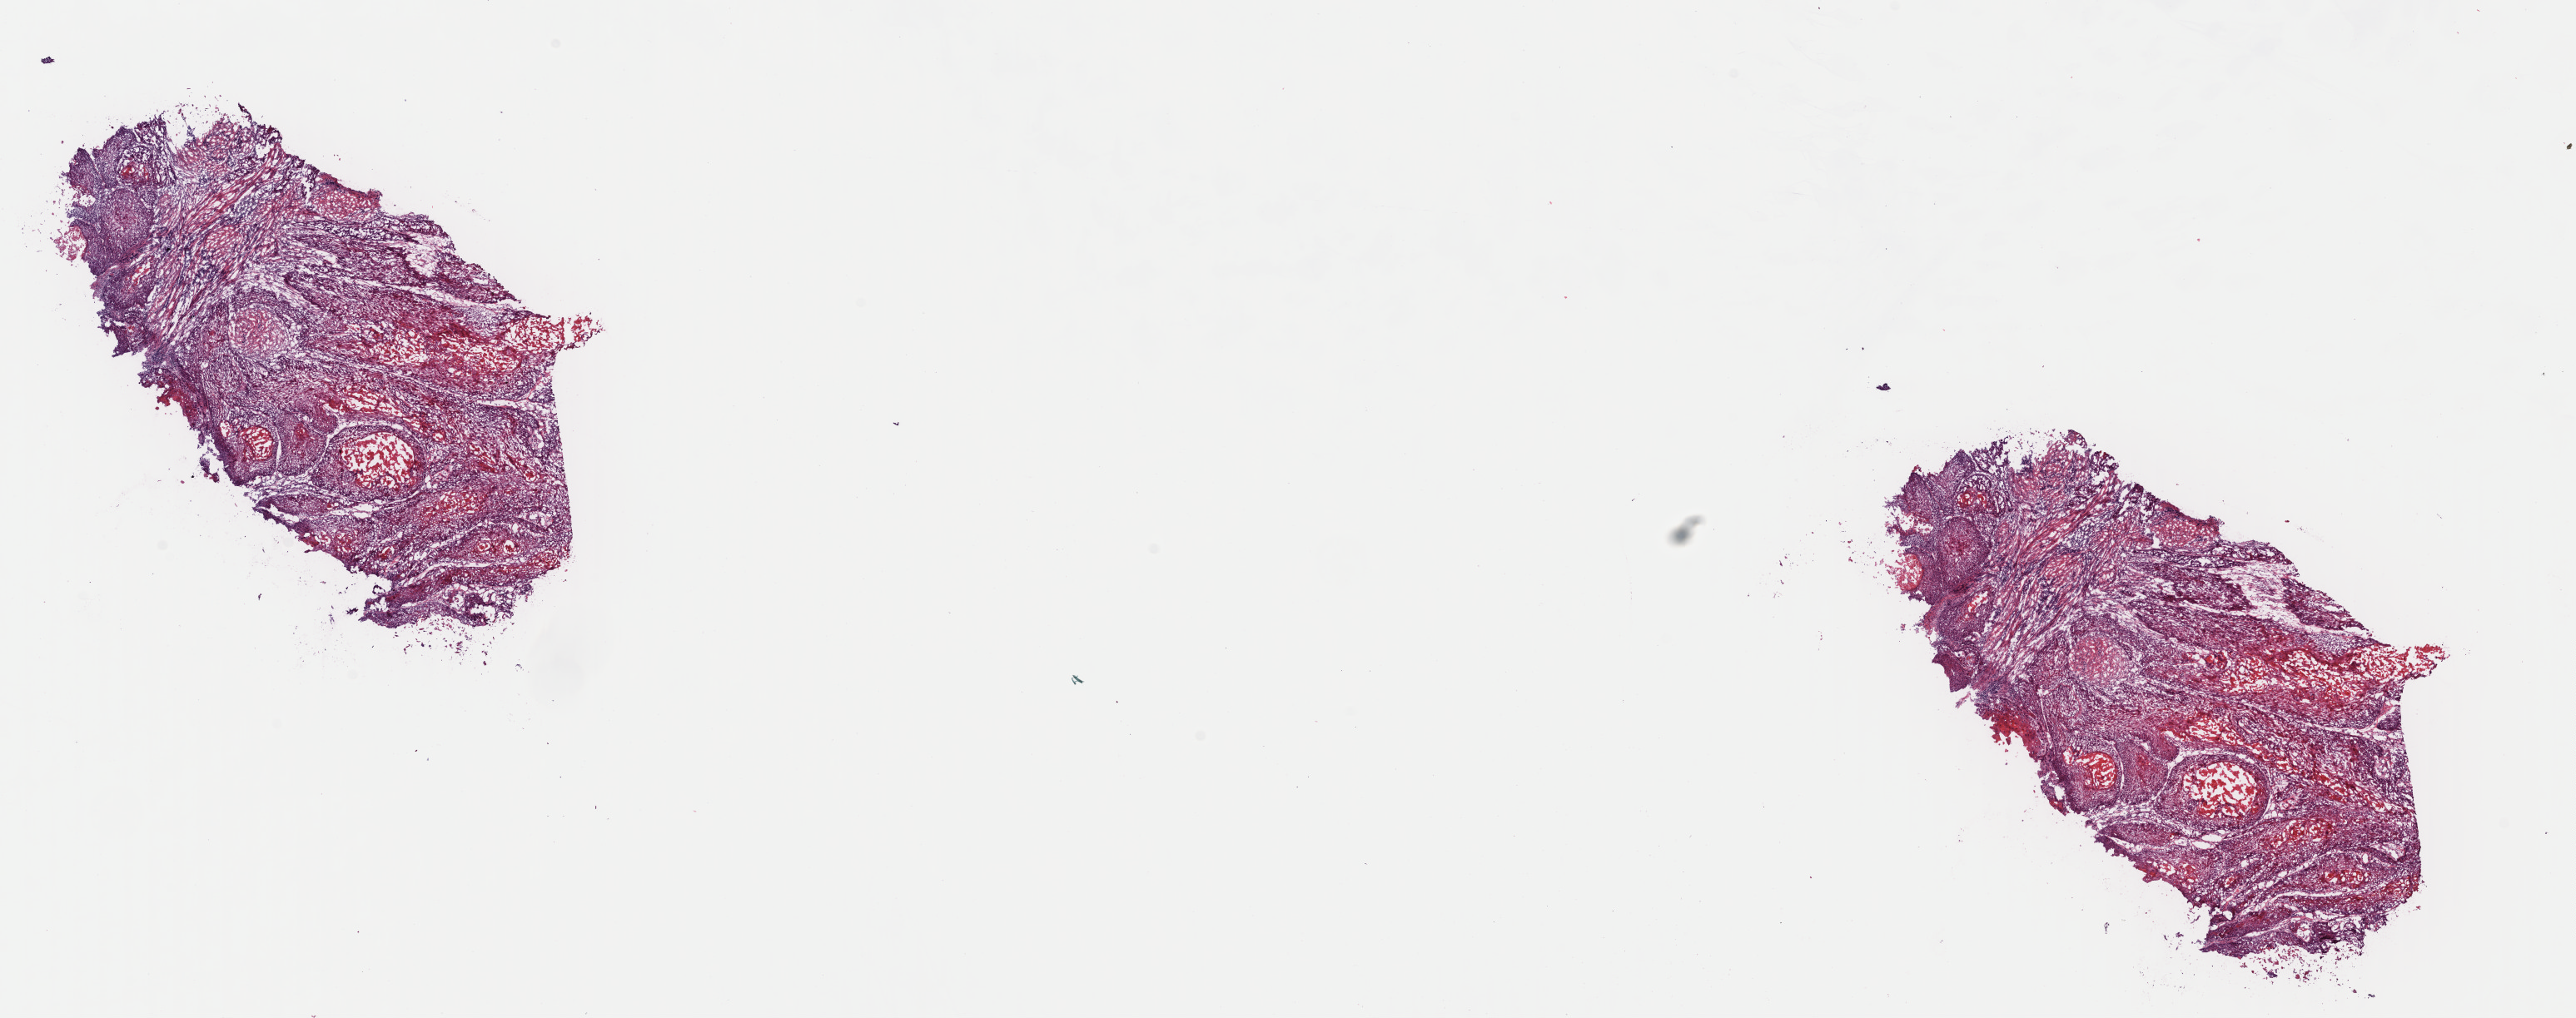
H&E whole-slide image — shown as a low-resolution overview of the whole scanned area (about 24.4 x 9.6 mm); frozen section; head and neck, primary tumour sample. Male patient; age at initial diagnosis 55 years. Histologic grade: G1 (well differentiated). Pathologist review of this section (percent, as recorded): tumour cells 75%, tumour nuclei 75%, normal cells 0%, stromal cells 25%, necrosis 0%. Inflammatory infiltration, as recorded: lymphocyte infiltration 10%, monocyte infiltration 0%, neutrophil infiltration 0%.
- AJCC pathologic stage: III (7th edition)
- laterality: left
- pathologic diagnosis: Squamous cell carcinoma, NOS (tongue, NOS)